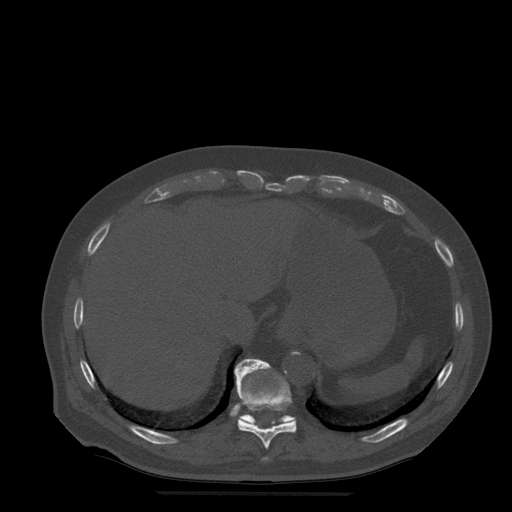
CT including the spine, one axial slice. Slice 262 of 522 in the series (ordered by position). Bone window (W 1800 / L 400 HU). 1.25 mm slice thickness. 512 × 512 image matrix, field of view 420 × 420 mm. Patient age 72 years. Case-level facts recorded for this patient, not image findings: primary cancer: prostate.
Outlined on this slice (semi-automatic segmentation, software-assisted and operator-edited):
- T10 vertebra: bounding box [x1, y1, x2, y2] px = [235, 362, 297, 449]
- T11 vertebra: [235, 359, 296, 426]
- T9 vertebra: [263, 458, 268, 460]